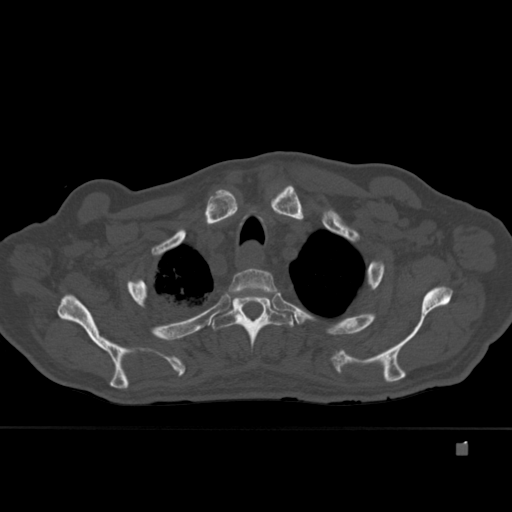
CT including the spine, one axial slice. Position 338 of 451 along the scan axis. Bone window (W 1800 / L 400 HU). 1.5 mm slice thickness. 512 × 512 image matrix. Patient: male, 75 years. Case-level facts recorded for this patient, not image findings: primary cancer: prostate.
Structures marked on this image (semi-automatic segmentation, software-assisted and operator-edited):
- T2 vertebra: bounding box <225,268,281,310> (left, top, right, bottom; pixels)
- T3 vertebra: <210,295,294,348>